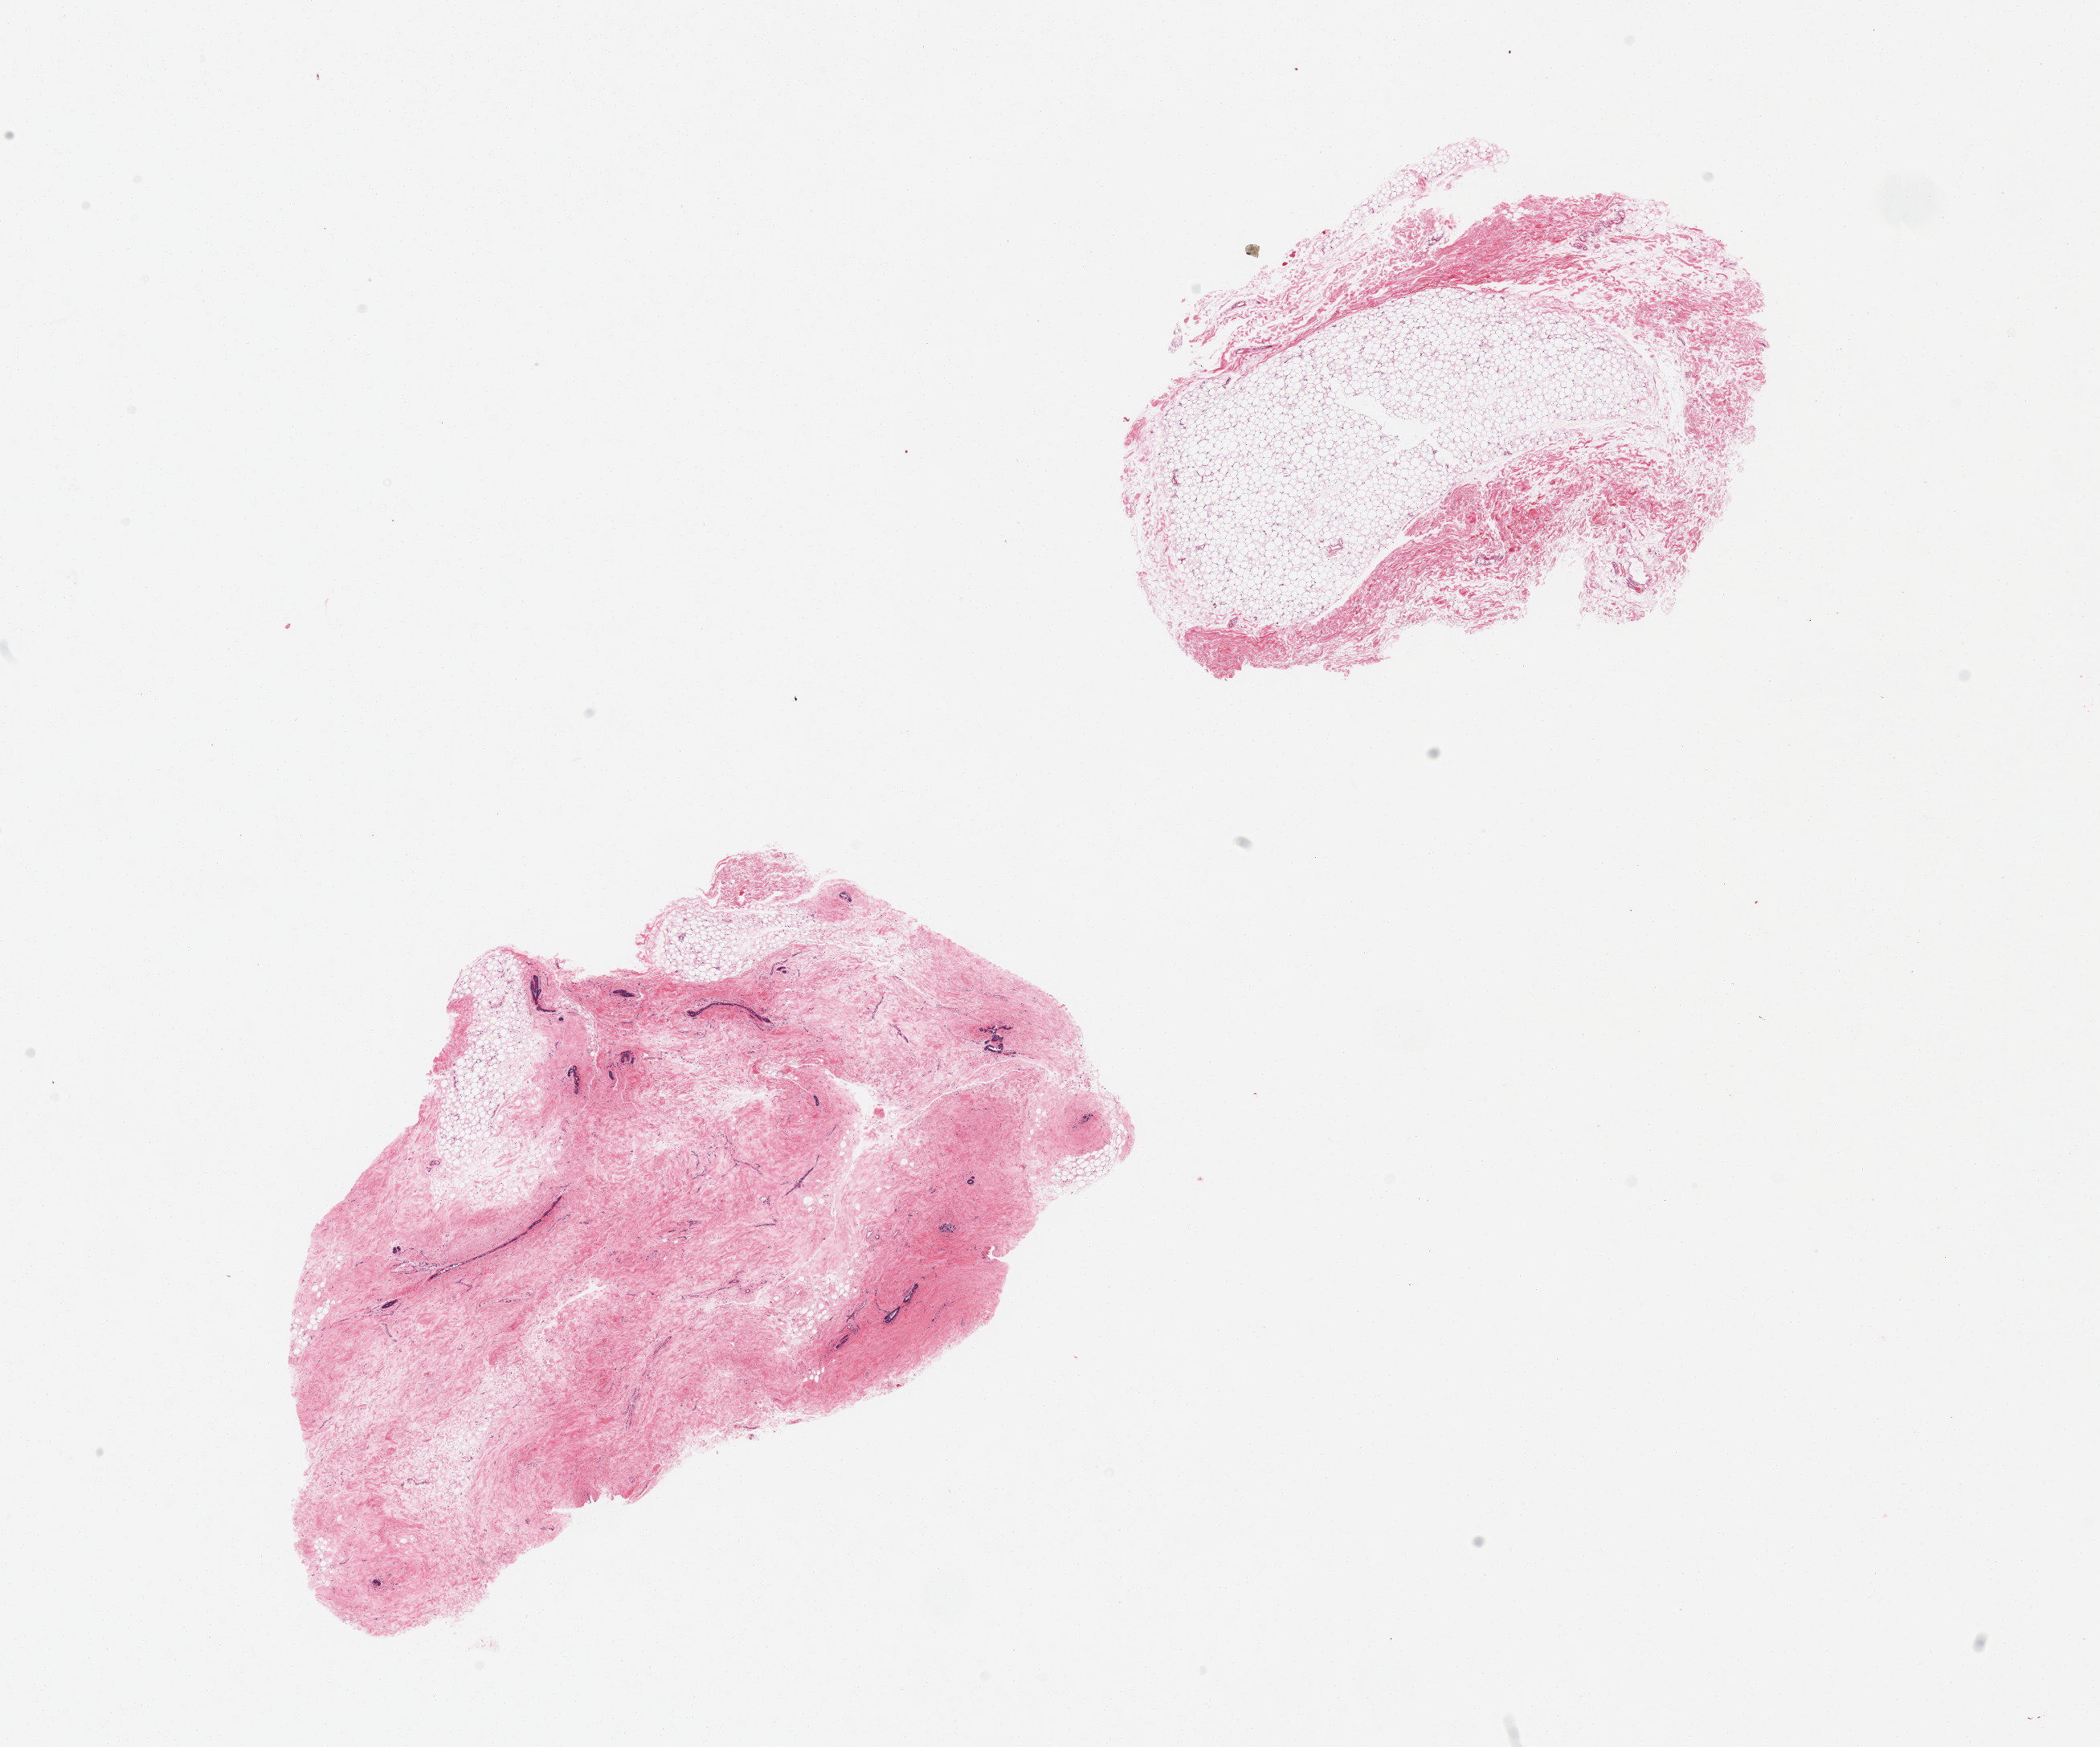
Digitized haematoxylin and eosin-stained section, a low-resolution overview of the entire scanned area, about 20.7 x 17.2 mm. PAXgene-fixed paraffin-embedded (PFPE) section. Target tissue: breast. Donor tissue sample. Donor sex: male.
Review note (as recorded): 2 pieces, gynecomastoid stromal hyperplasia; Rep ductal elements.